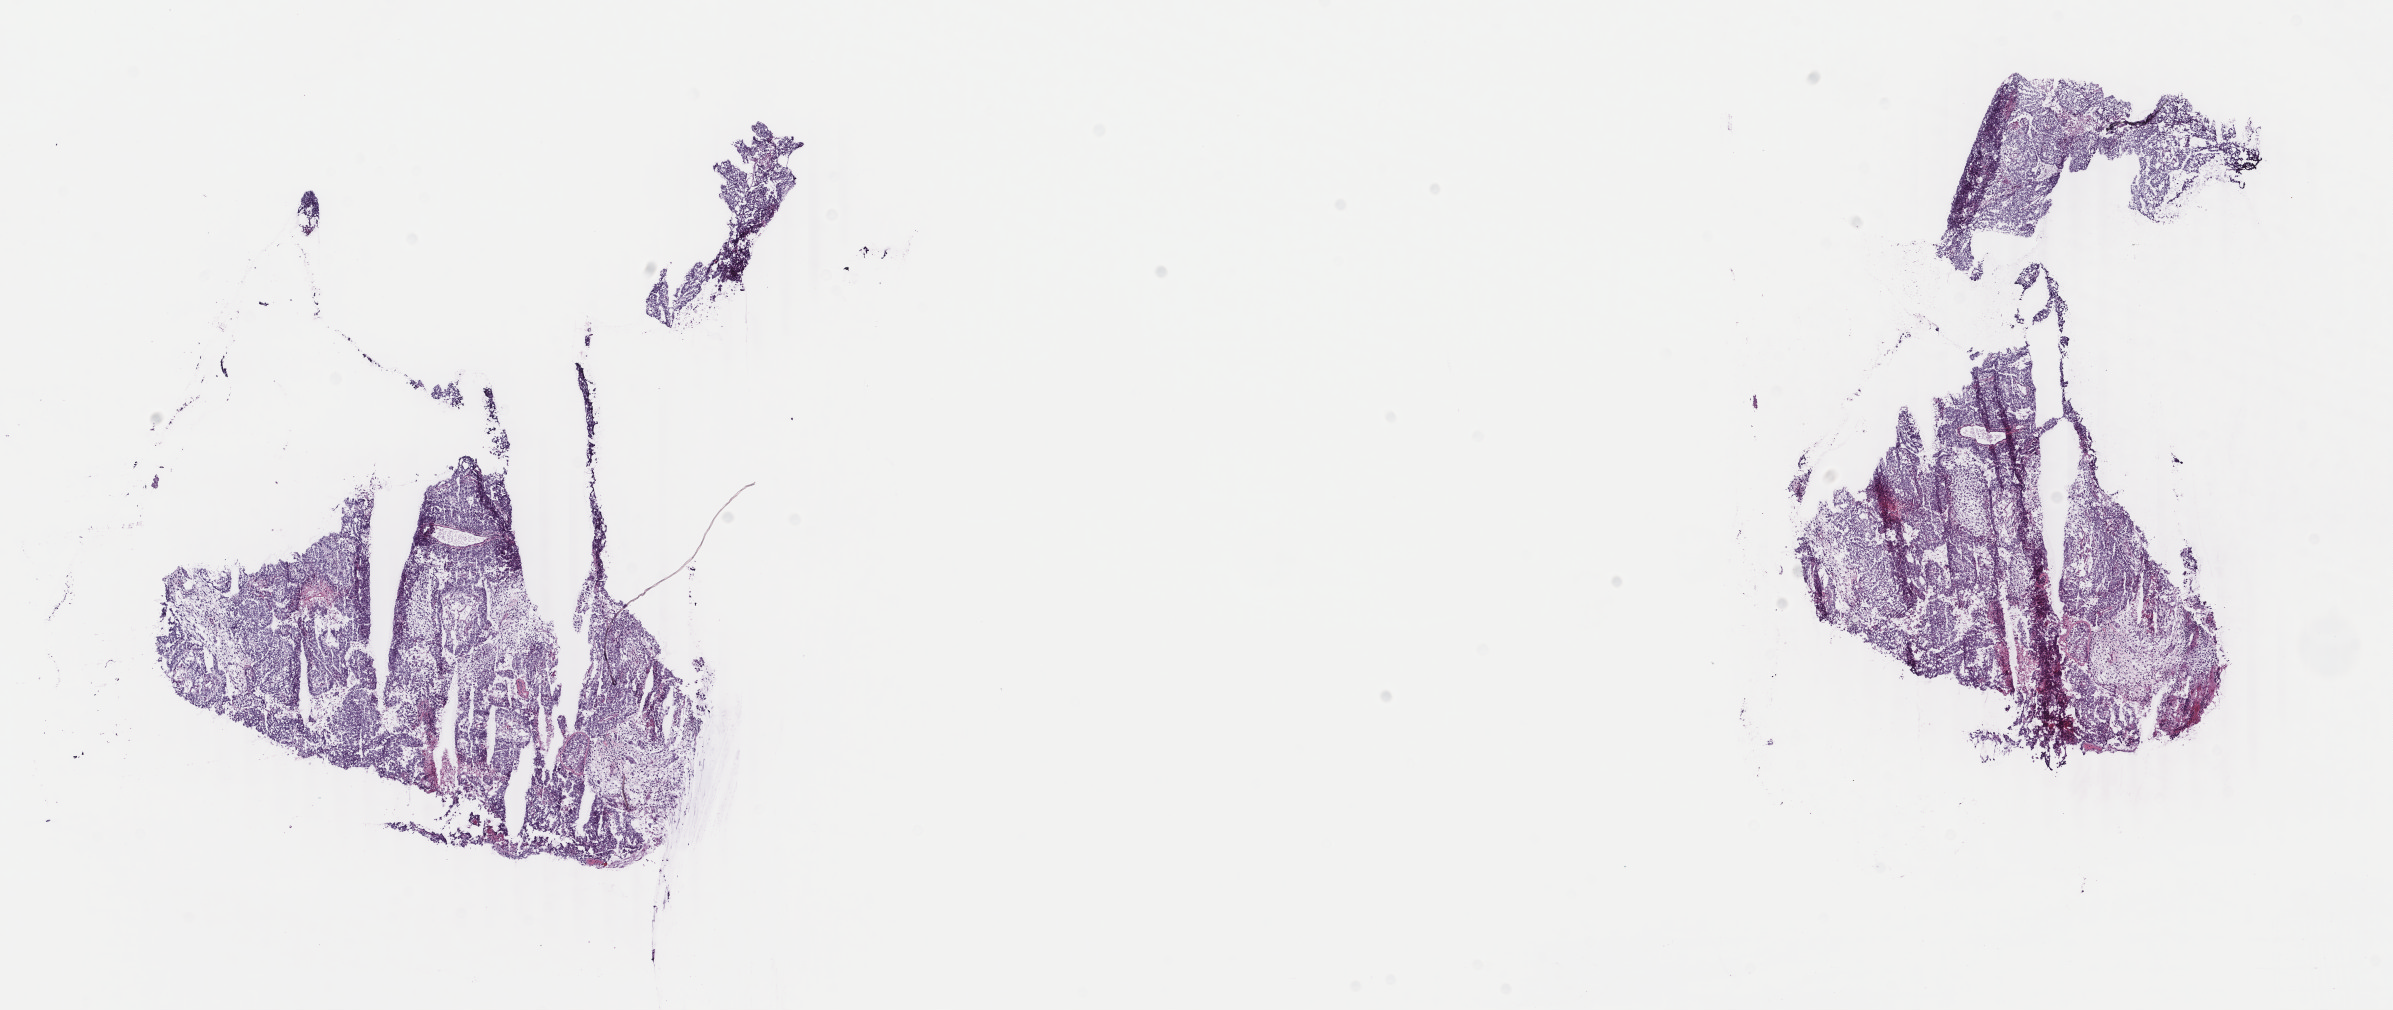
Digitized H&E-stained tissue section (whole slide) — whole scanned area (about 19.0 x 8.0 mm, acquisition: 40x scan) shown as a low-resolution overview. Patient sex: male. Slide review estimates, as recorded: tumour cells 100%, tumour nuclei 80%, normal cells 0%, stromal cells 0%, necrosis 0%. Inflammatory infiltration, as recorded: lymphocyte infiltration 3%, monocyte infiltration 0%, neutrophil infiltration 0%.
Specimen: frozen section; primary tumour sample from the testis.